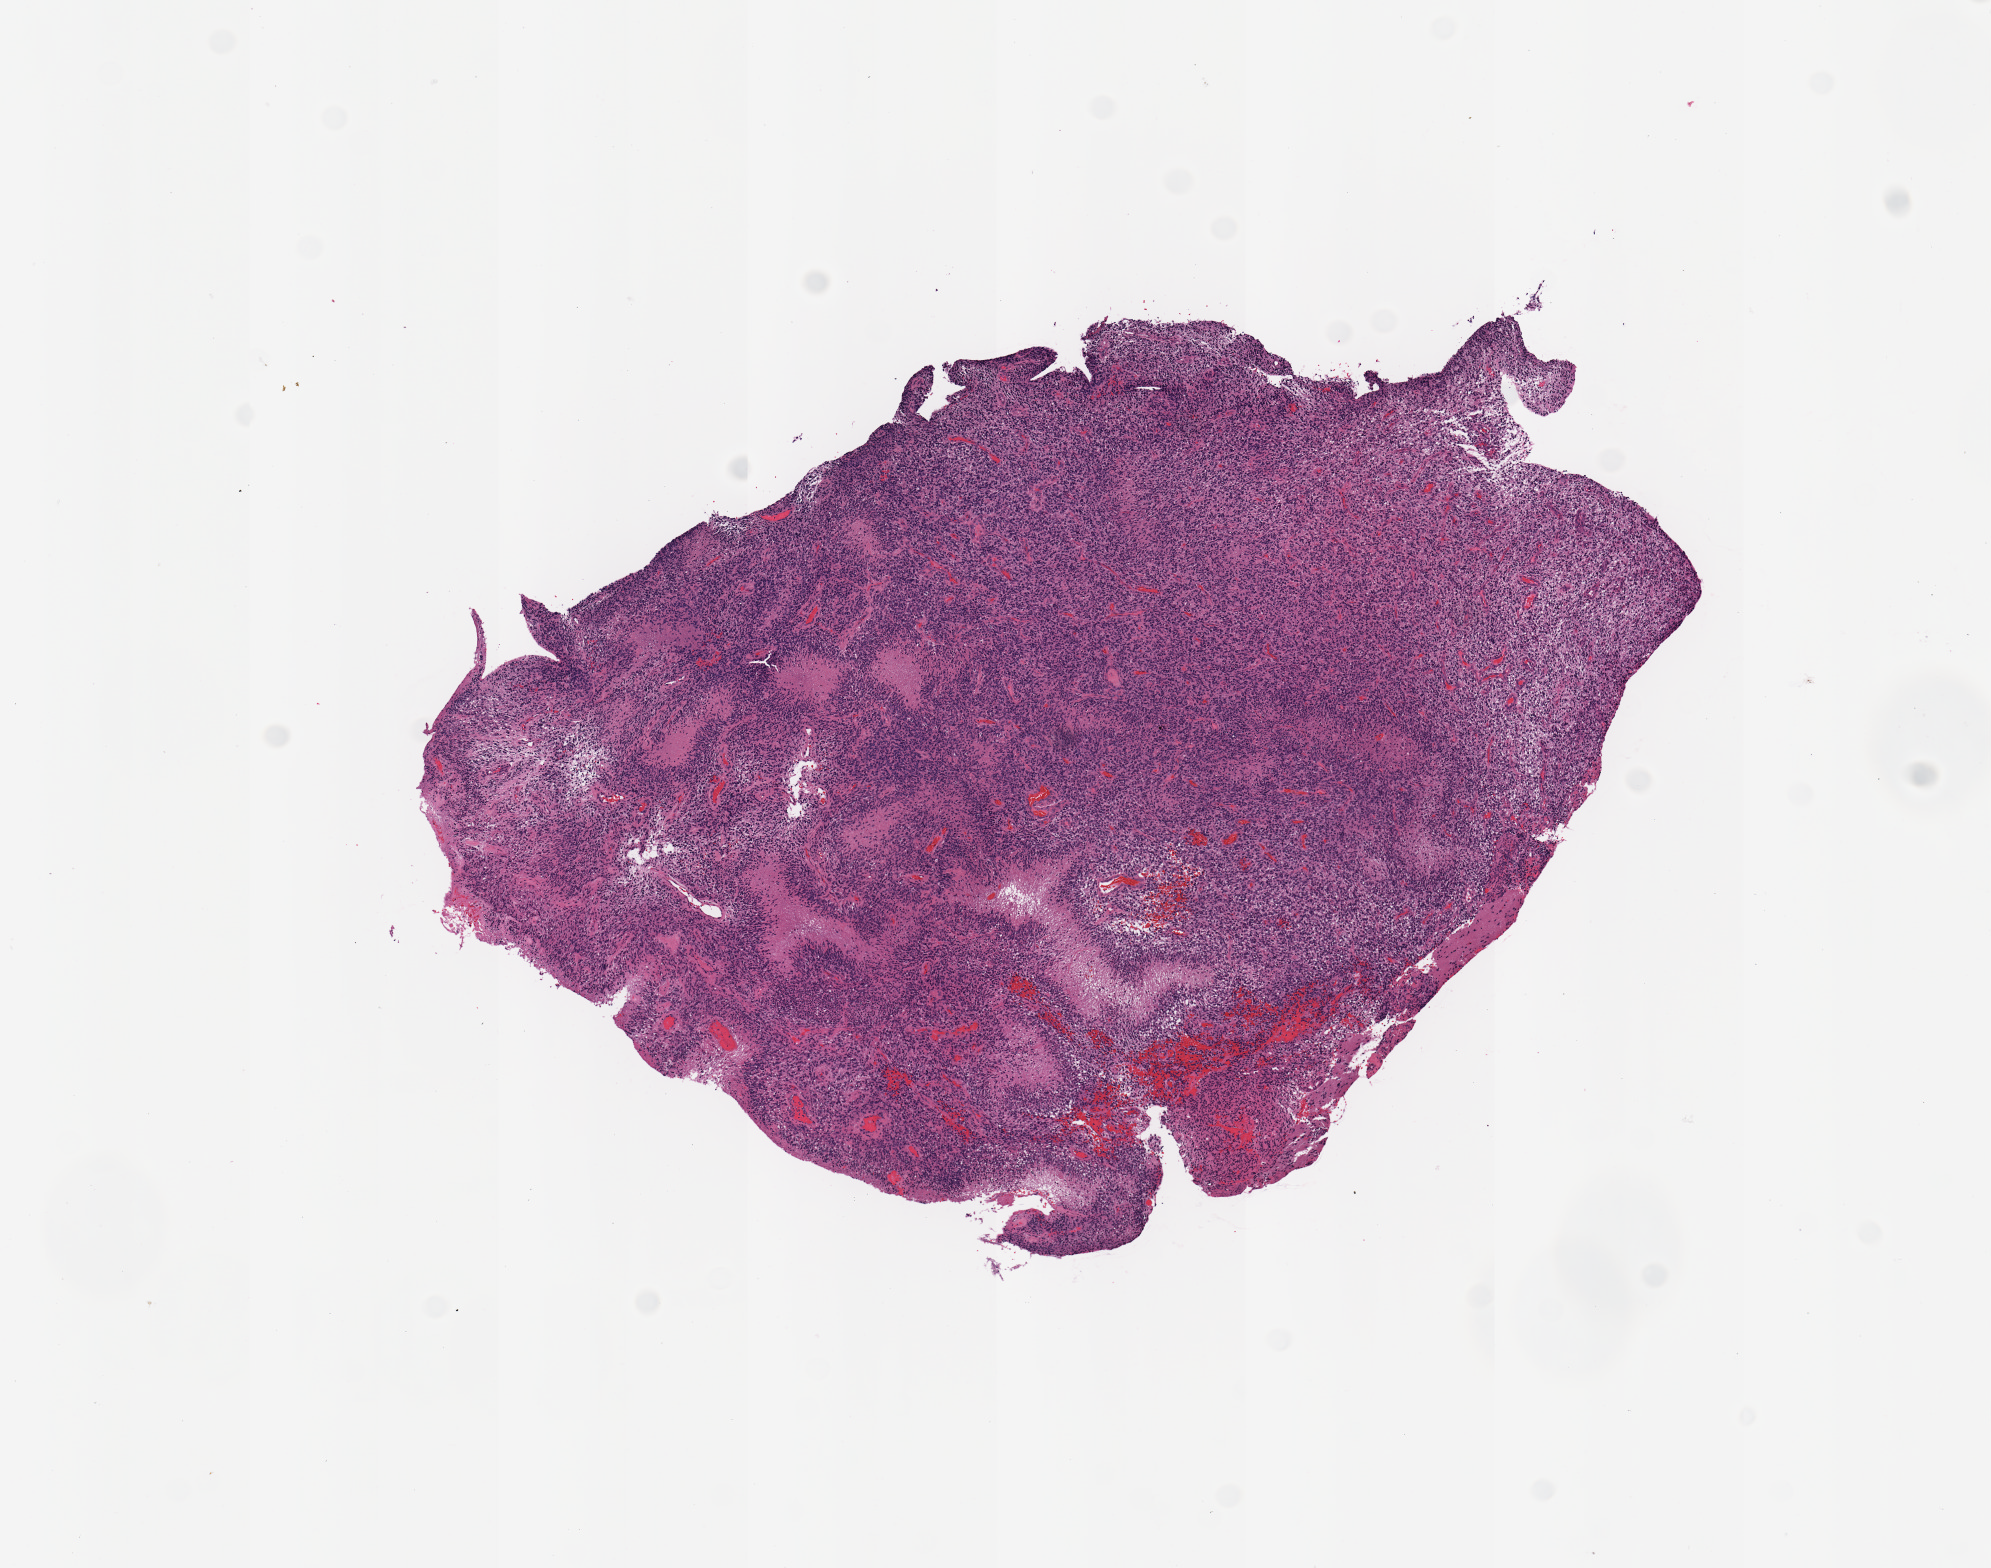
Digitized H&E-stained tissue section (whole slide), low-resolution overview of the scanned area, about 7.9 x 6.2 mm. Tumour tissue sample, sampled site: brain. 44-year-old female patient. Composition of this section per pathologist review: tumour nuclei 75%, necrosis 15%.
Diagnosis: Glioblastoma.